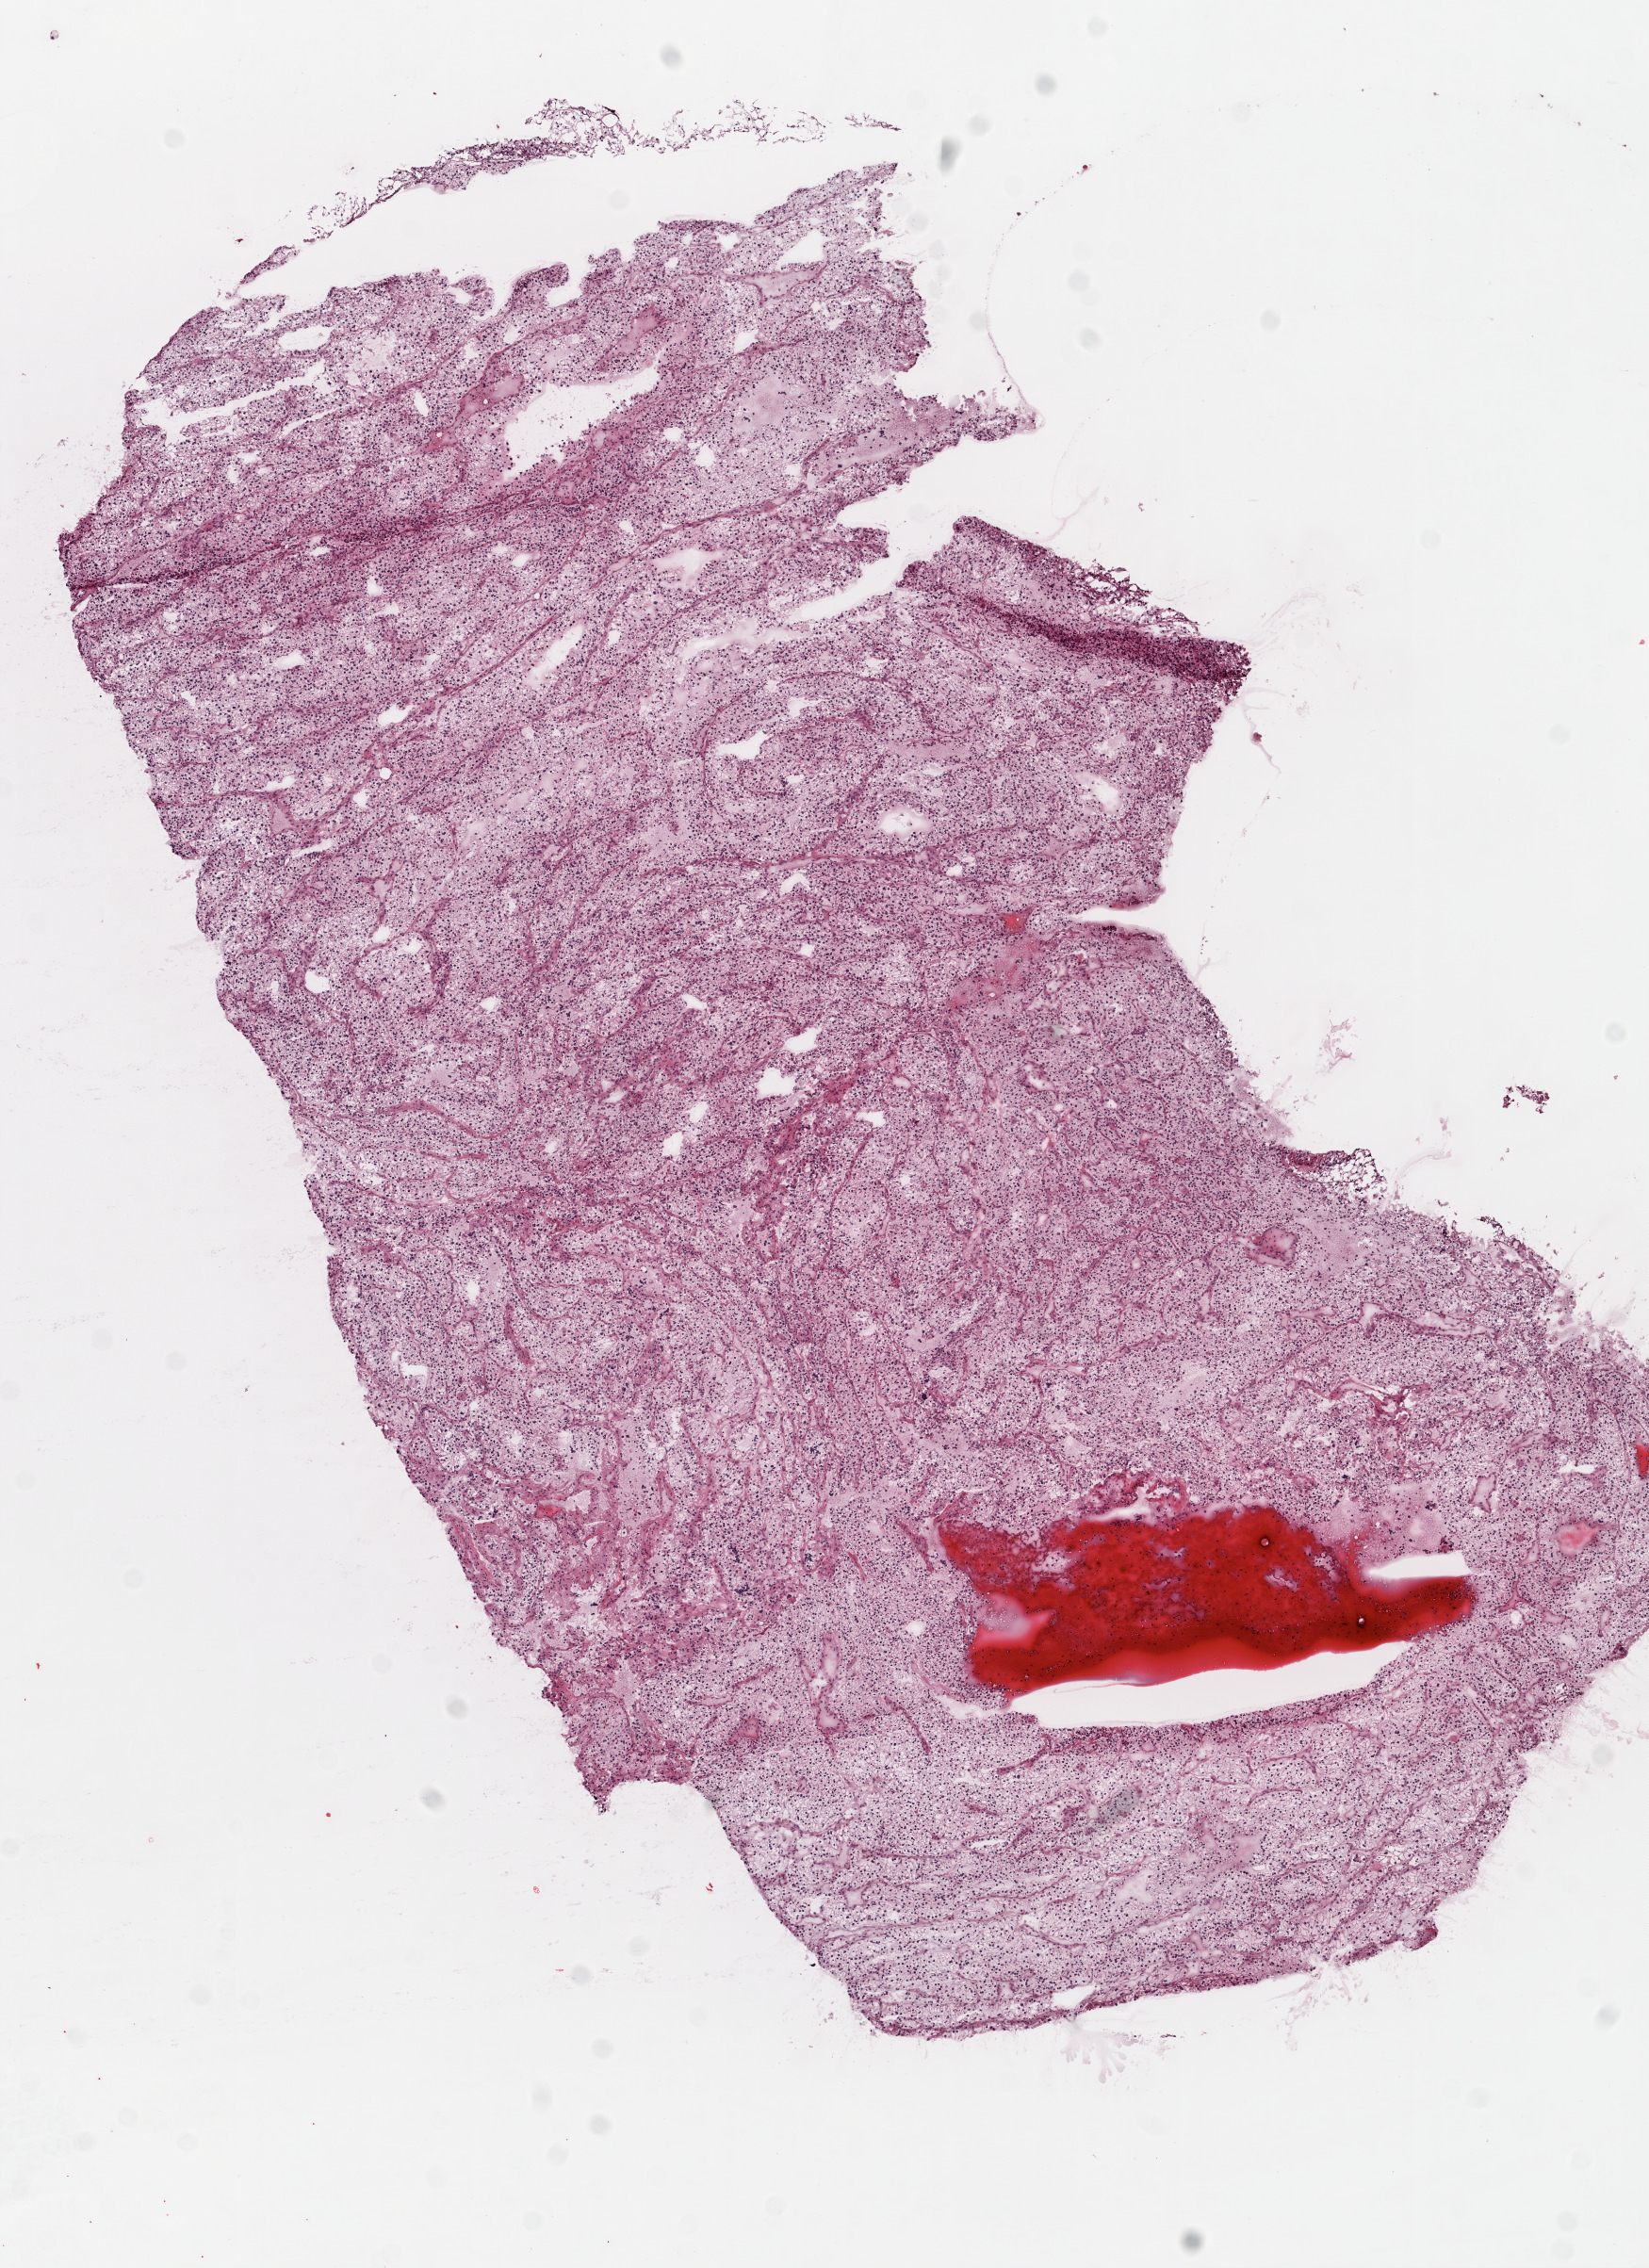
Whole-slide histology image, H&E, a low-resolution overview of the entire scanned area, about 7.0 x 9.7 mm (from a 20x scan); frozen section from the top of the tissue portion; kidney, primary tumour sample. Female patient; age at initial diagnosis 72 years. Pathologist review of this section (percent, as recorded): tumour cells 100%, tumour nuclei 95%.
Diagnosis: Clear cell adenocarcinoma, NOS.